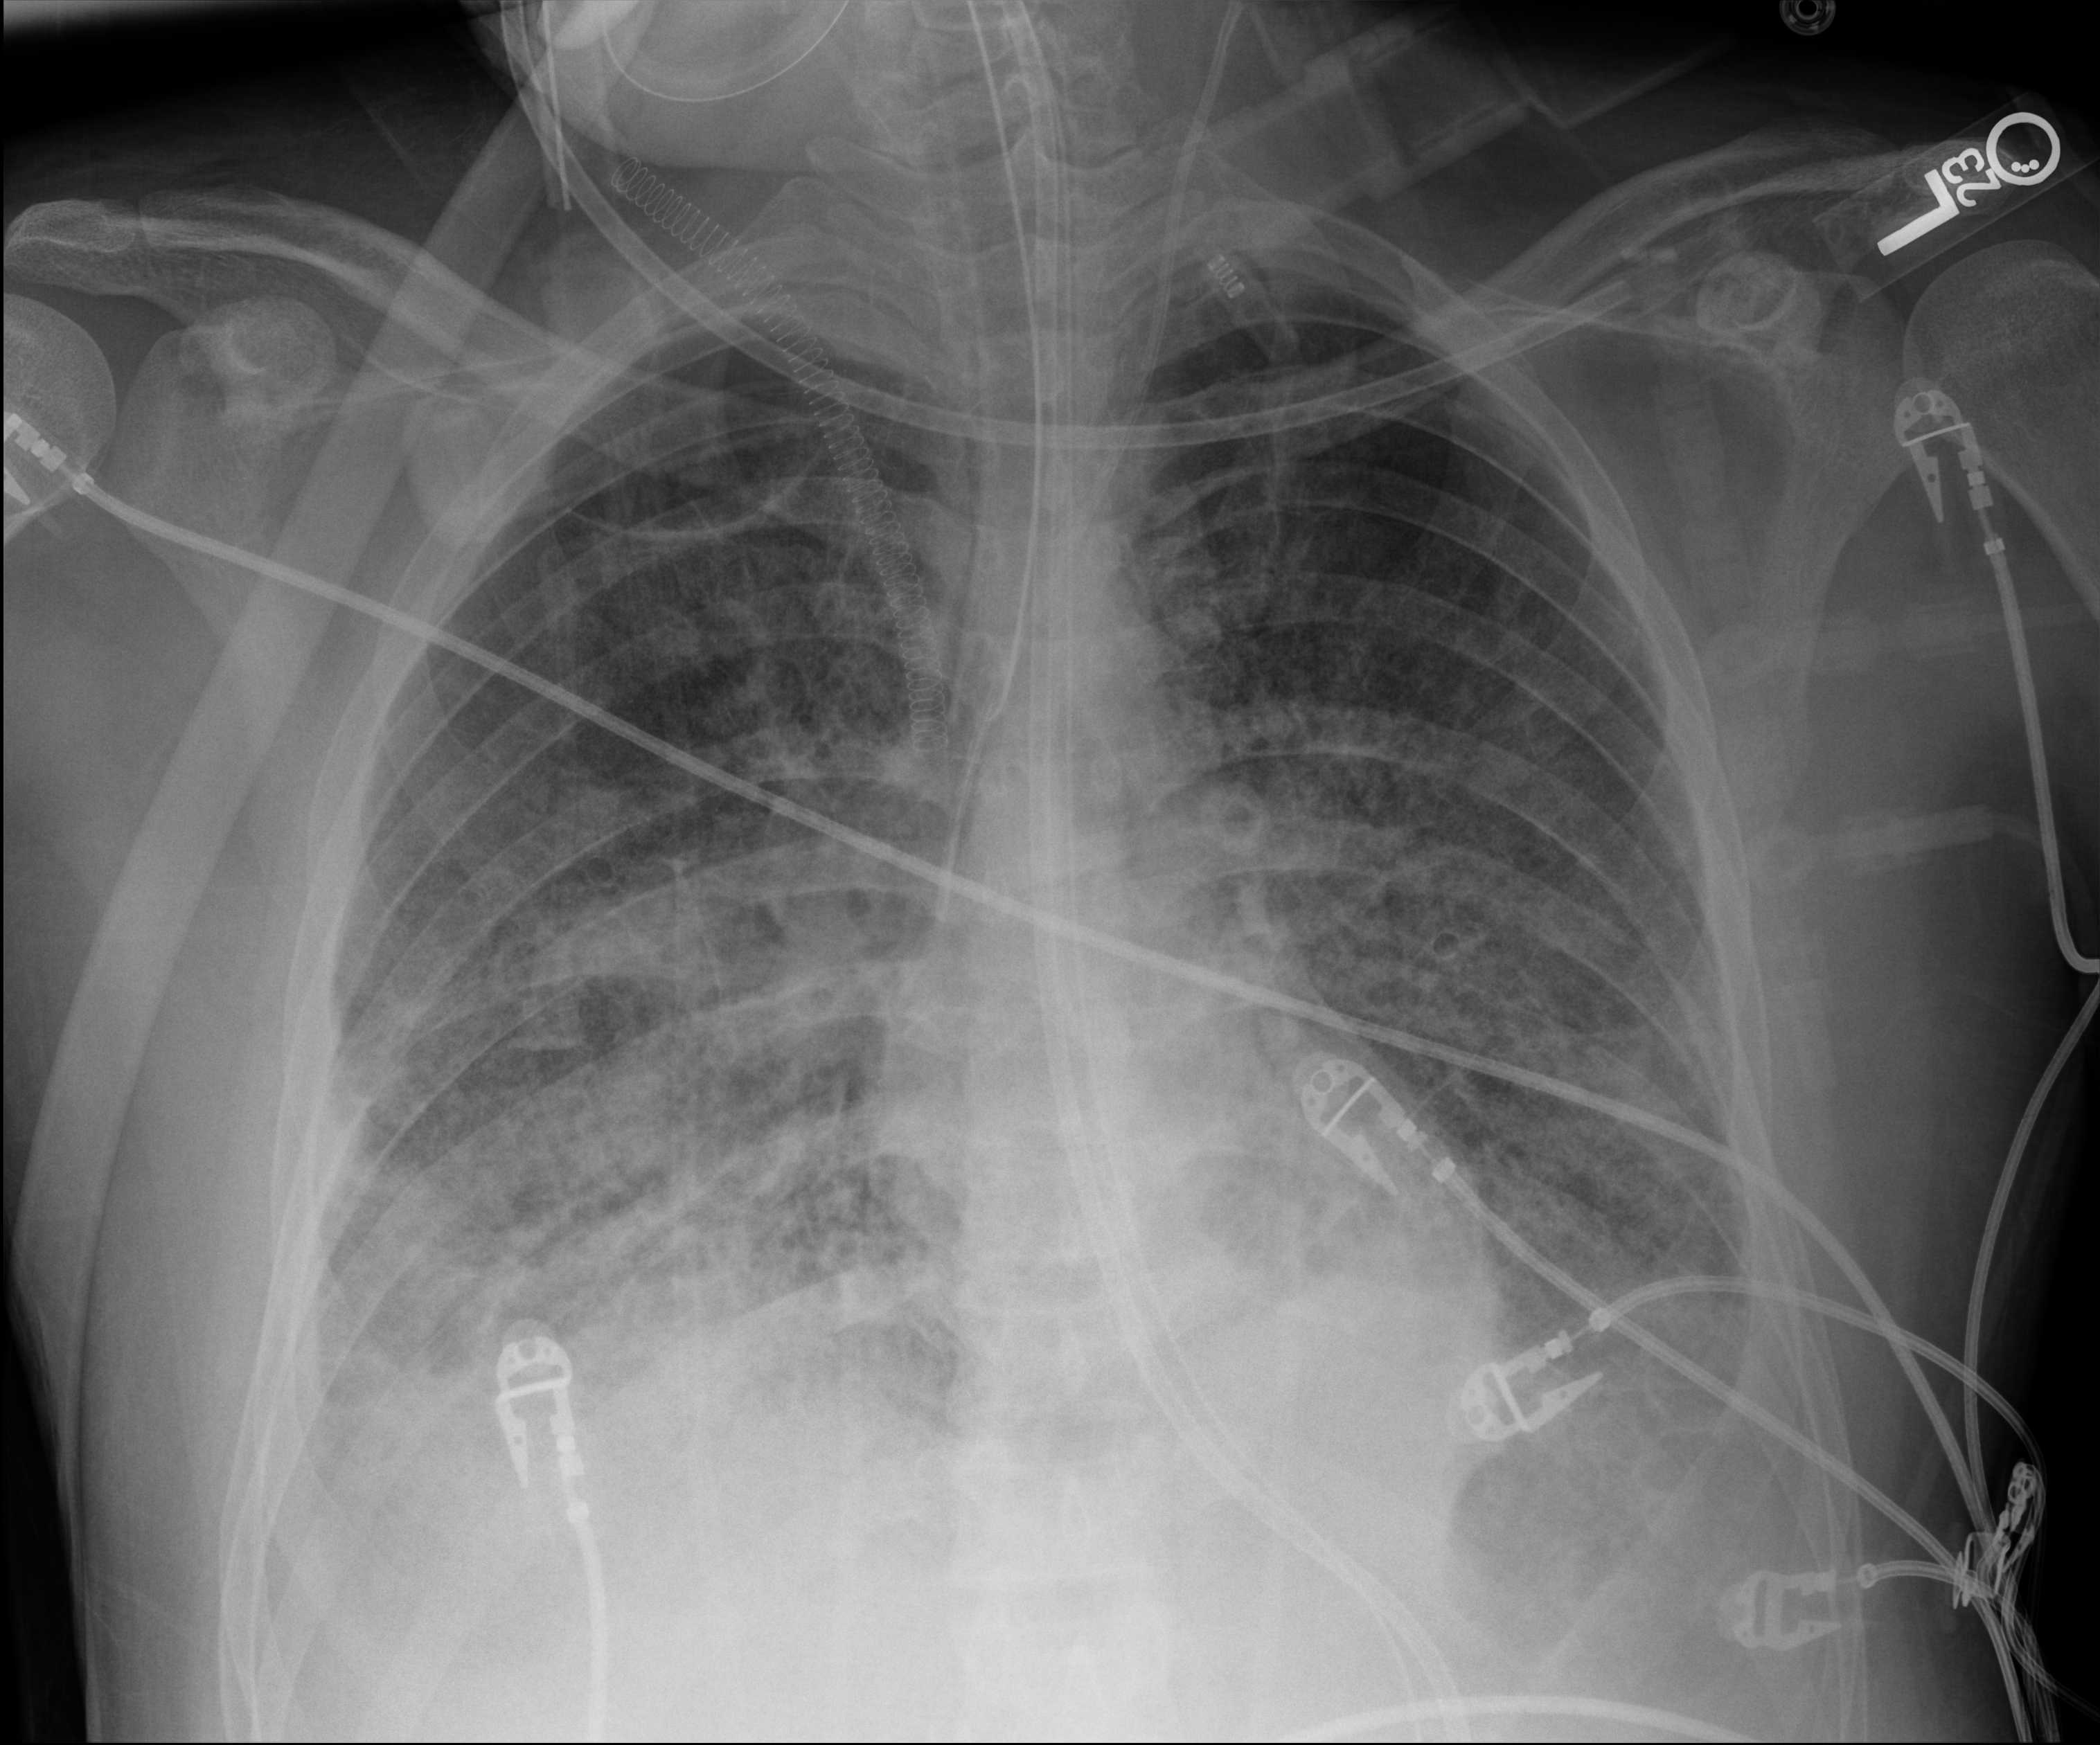
Portable chest radiograph, anteroposterior (AP) projection. Adult patient hospitalised with COVID-19, age 18–59 years.
Admission-level facts for this patient (not findings on this image; timing relative to this image not recorded):
- mechanically ventilated during this hospital stay: yes
- admitted to intensive care during this hospital stay: yes